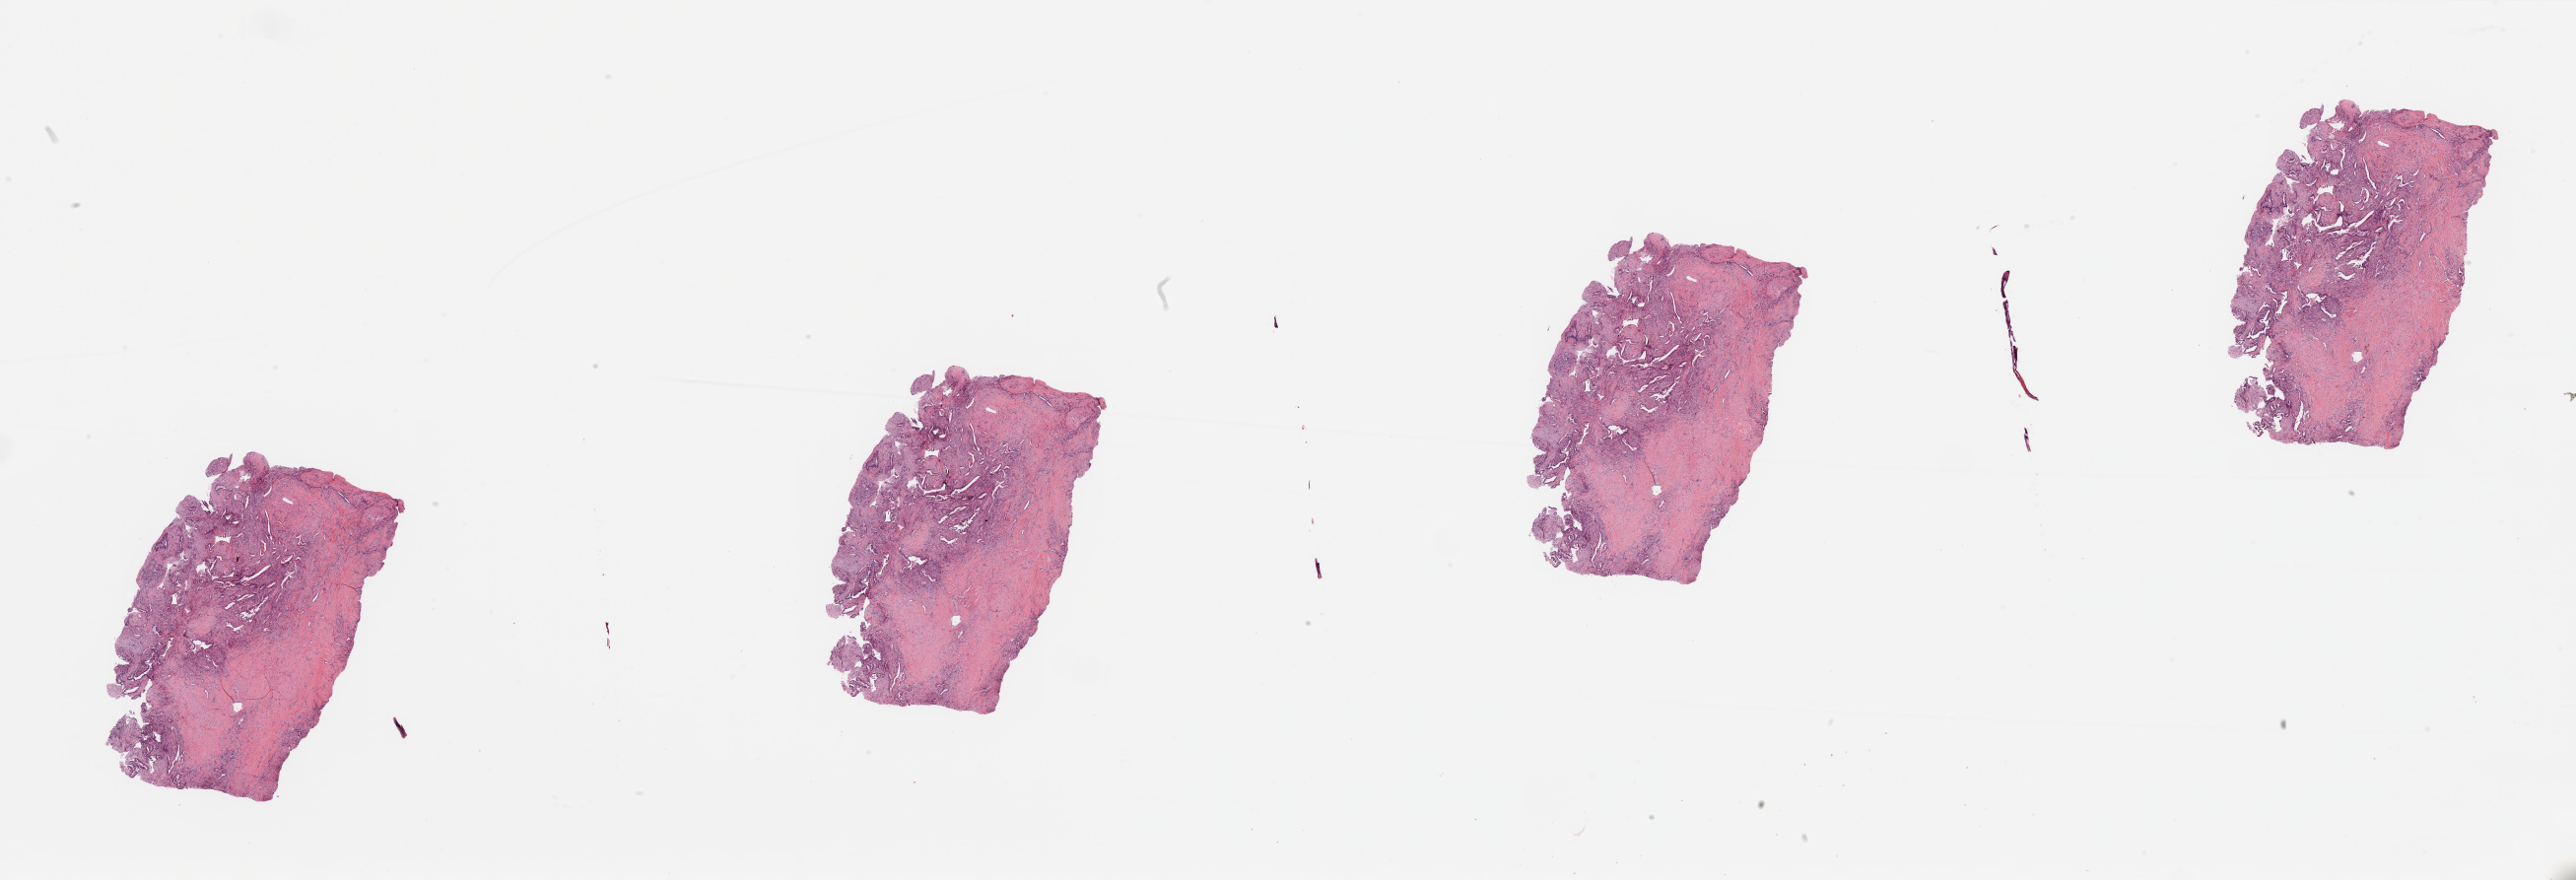
H&E whole-slide image — shown as a low-resolution overview of the whole scanned area (about 41.3 x 14.1 mm), tumour tissue sample, pancreas. Patient: male, age 62 years. Histologic grade: G2 (moderately differentiated).
AJCC pathologic stage: IIB. Primary tumour site (as recorded): head. Histologic diagnosis: Infiltrating duct carcinoma, NOS.